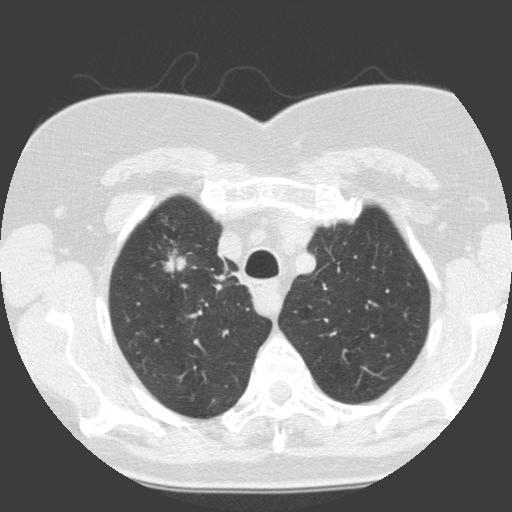
Low-dose screening chest CT, axial slice; first (baseline) screen; lung window (W 1500 / L -600 HU); 2 mm slice thickness; slice 28 of 146 in the series; 512 × 512 image matrix, field of view 300 × 300 mm. Female participant, aged 68 years at enrolment. Current smoker at enrolment.
Lesion marked by an expert reader, box from (x=153, y=243) to (x=199, y=286) px. The exam's reader record, not a measurement of the box and not confirmed to be the same lesion: non-calcified nodule or mass ≥4 mm, right upper lobe, 19 × 12 mm, smooth margins, soft tissue attenuation. Official screen result: positive, change unspecified: nodule(s) >= 4 mm or enlarging nodule(s), mass(es), or other non-specific abnormalities suspicious for lung cancer.